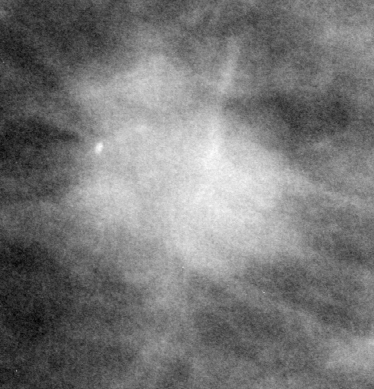
Region of interest cut from a scanned film mammogram (one marked finding); left breast; CC view.
Mass, shape oval, margins spiculated; BI-RADS assessment category 5; pathology (as recorded): malignant.